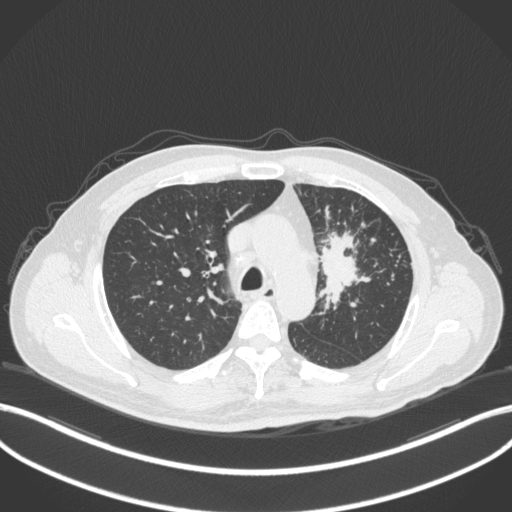
Chest CT, one axial slice; slice 248 of 386 in the series (ordered by position); 120 kVp; lung window (W 1500 / L -600 HU); 1 mm slice thickness; 512 × 512 image matrix, field of view 400 × 400 mm. Male patient, age 69 years. Case-level facts recorded for this patient, not image findings: clinical TNM (as recorded): T2a N2 M0.
Structures marked on this image (rectangle marked by the reading radiologist):
- lung tumour (recorded histology: adenocarcinoma): bounding box [x1, y1, x2, y2] px = [317, 222, 371, 311]